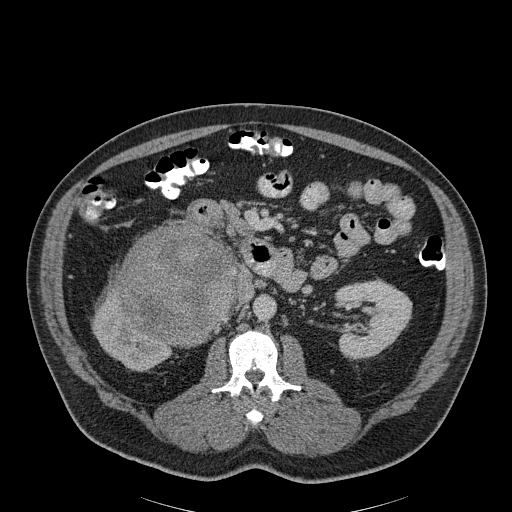
Contrast-enhanced abdominal CT, one axial slice. Slice 111 of 186 in the series (ordered by position). Reconstruction kernel B30f. Soft-tissue window (W 400 / L 40 HU). 512 × 512 image matrix, field of view 464 × 464 mm. Male patient, age 56 years. From the clinical record (not read from this slice): diagnosis: adrenocortical carcinoma; tumour side: right adrenal; tumour size at pathology: 18 cm; Ki-67 index: 2 %; stage (as recorded): 3.
Outlined on this slice (semi-automatically segmented with operator editing):
- mass: bounding box [x1, y1, x2, y2] px = [119, 229, 236, 346]